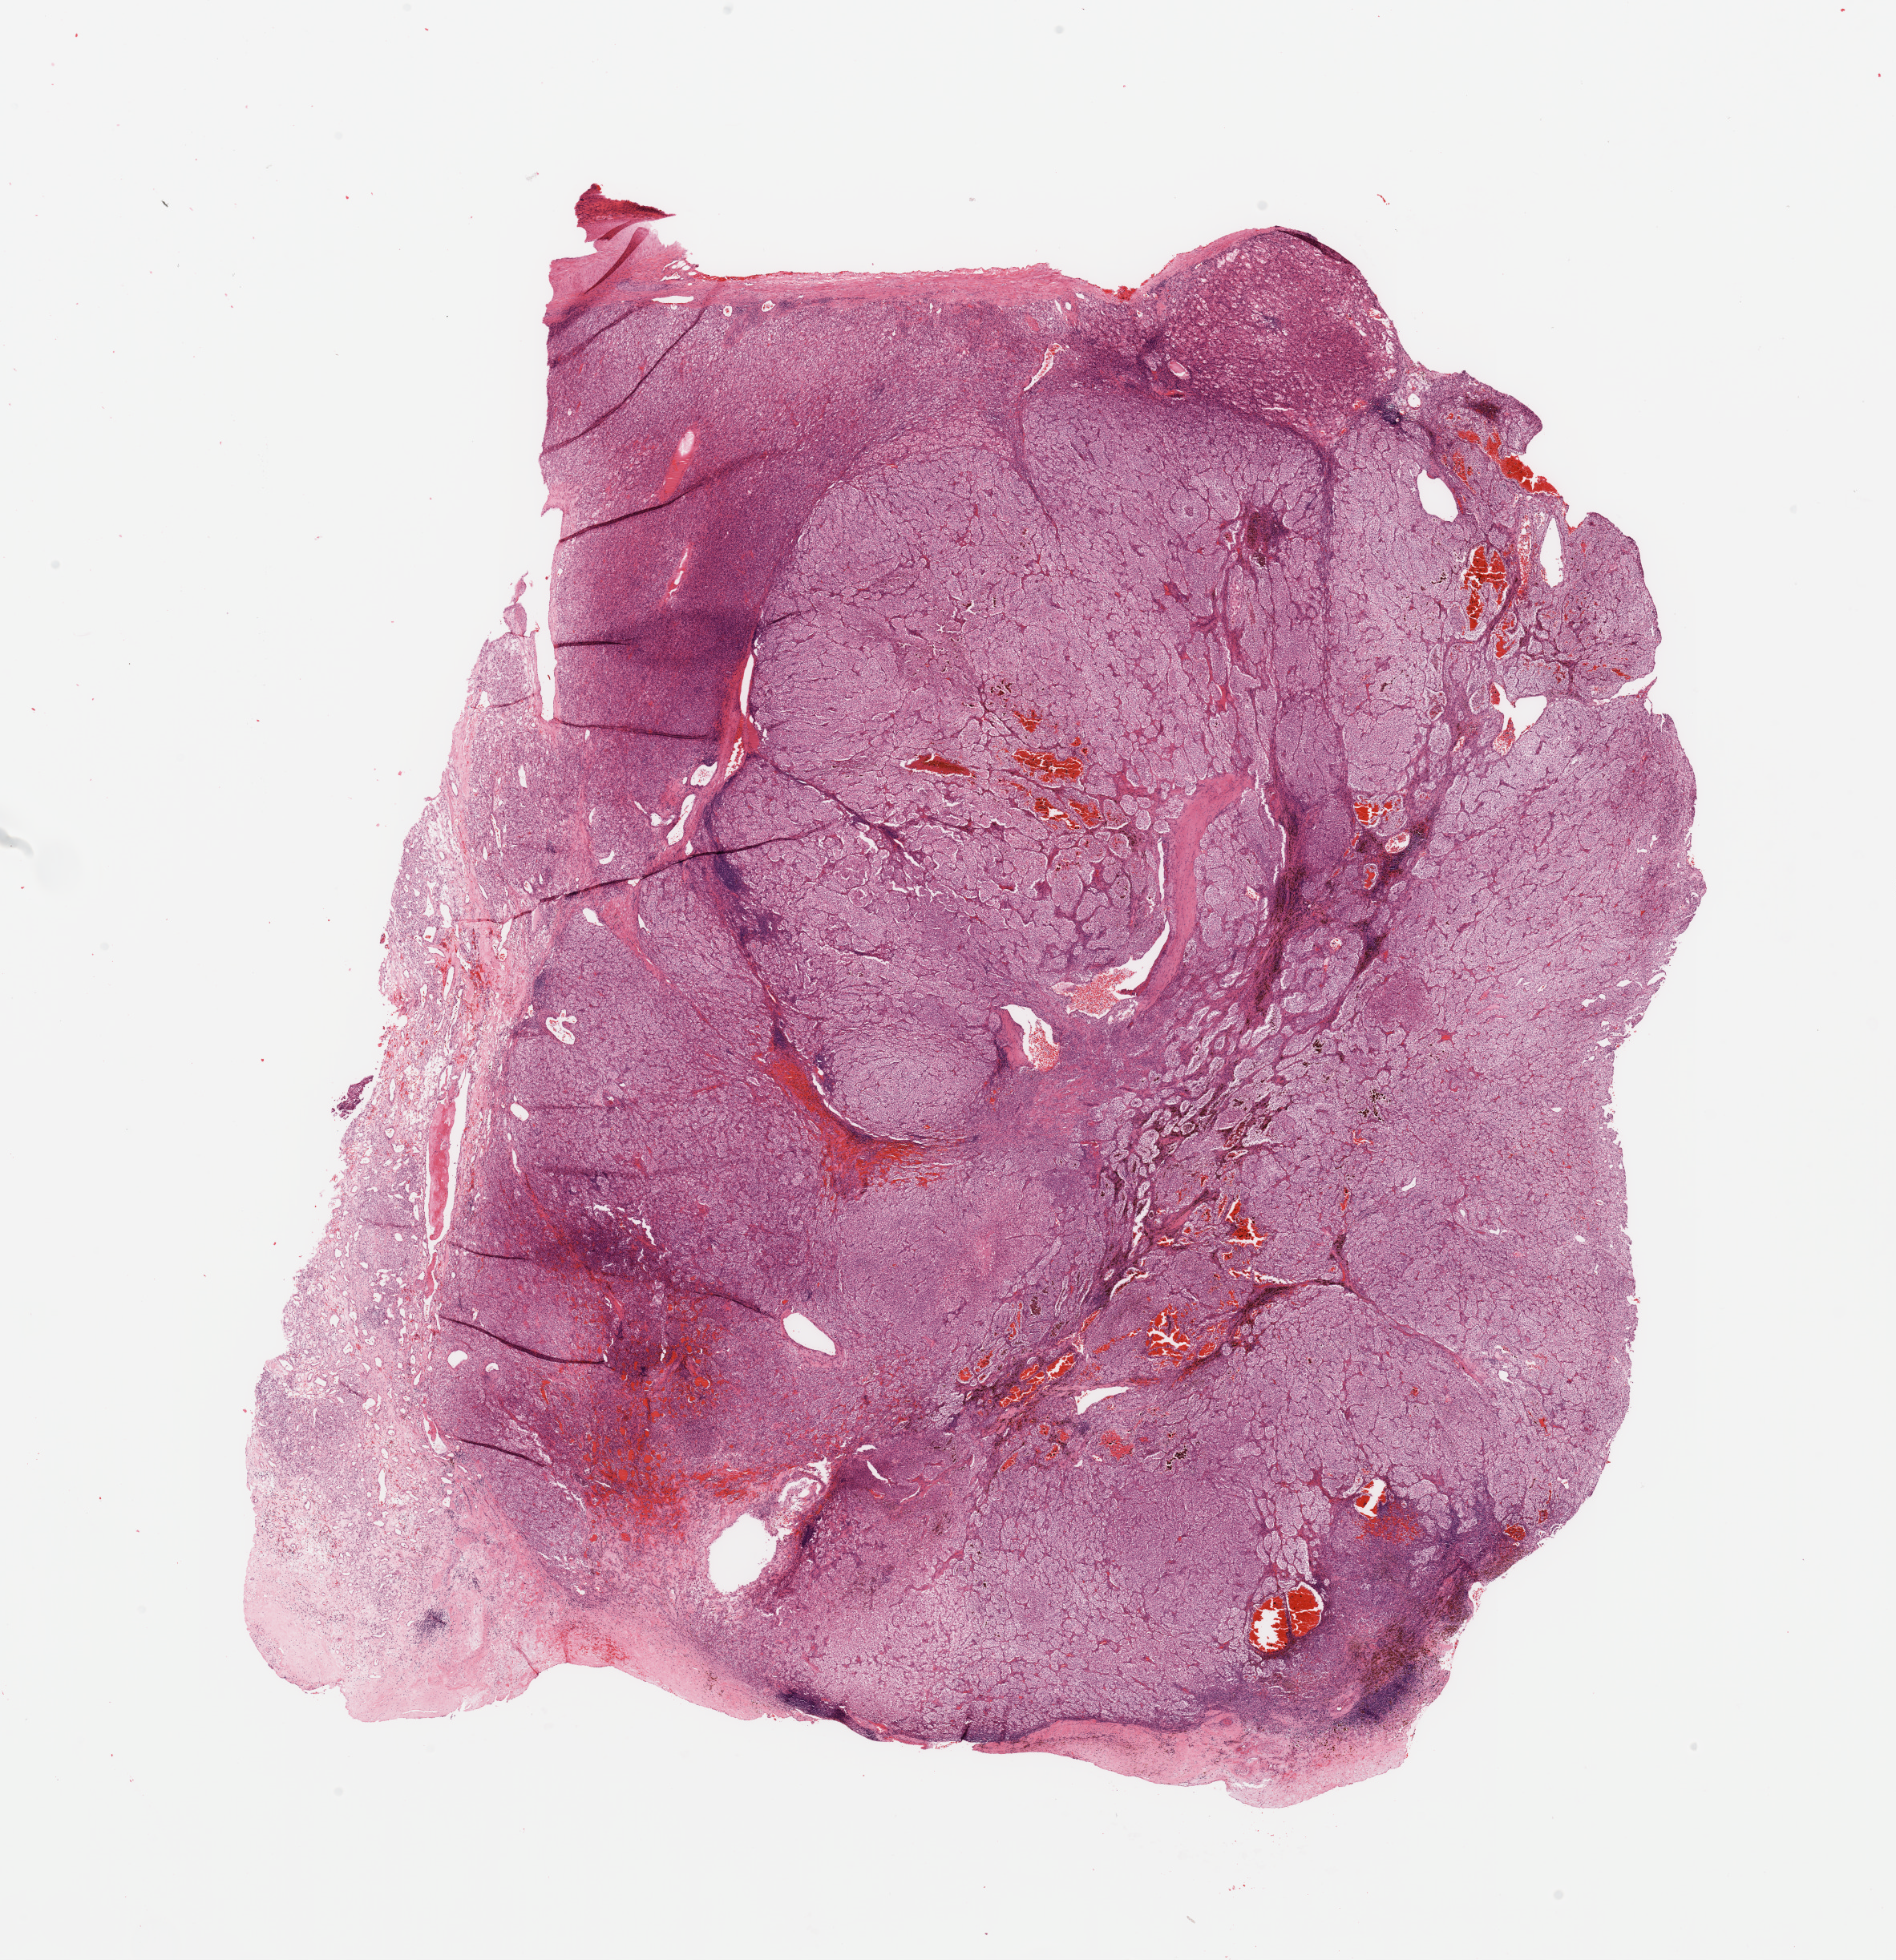
Whole-slide histology image, H&E-stained, shown as a low-resolution overview of the whole scanned area (about 18.7 x 19.3 mm, acquisition: 20x scan), tumour tissue sample, kidney. Male, 53 y/o.
Diagnosis: Renal cell carcinoma, NOS.